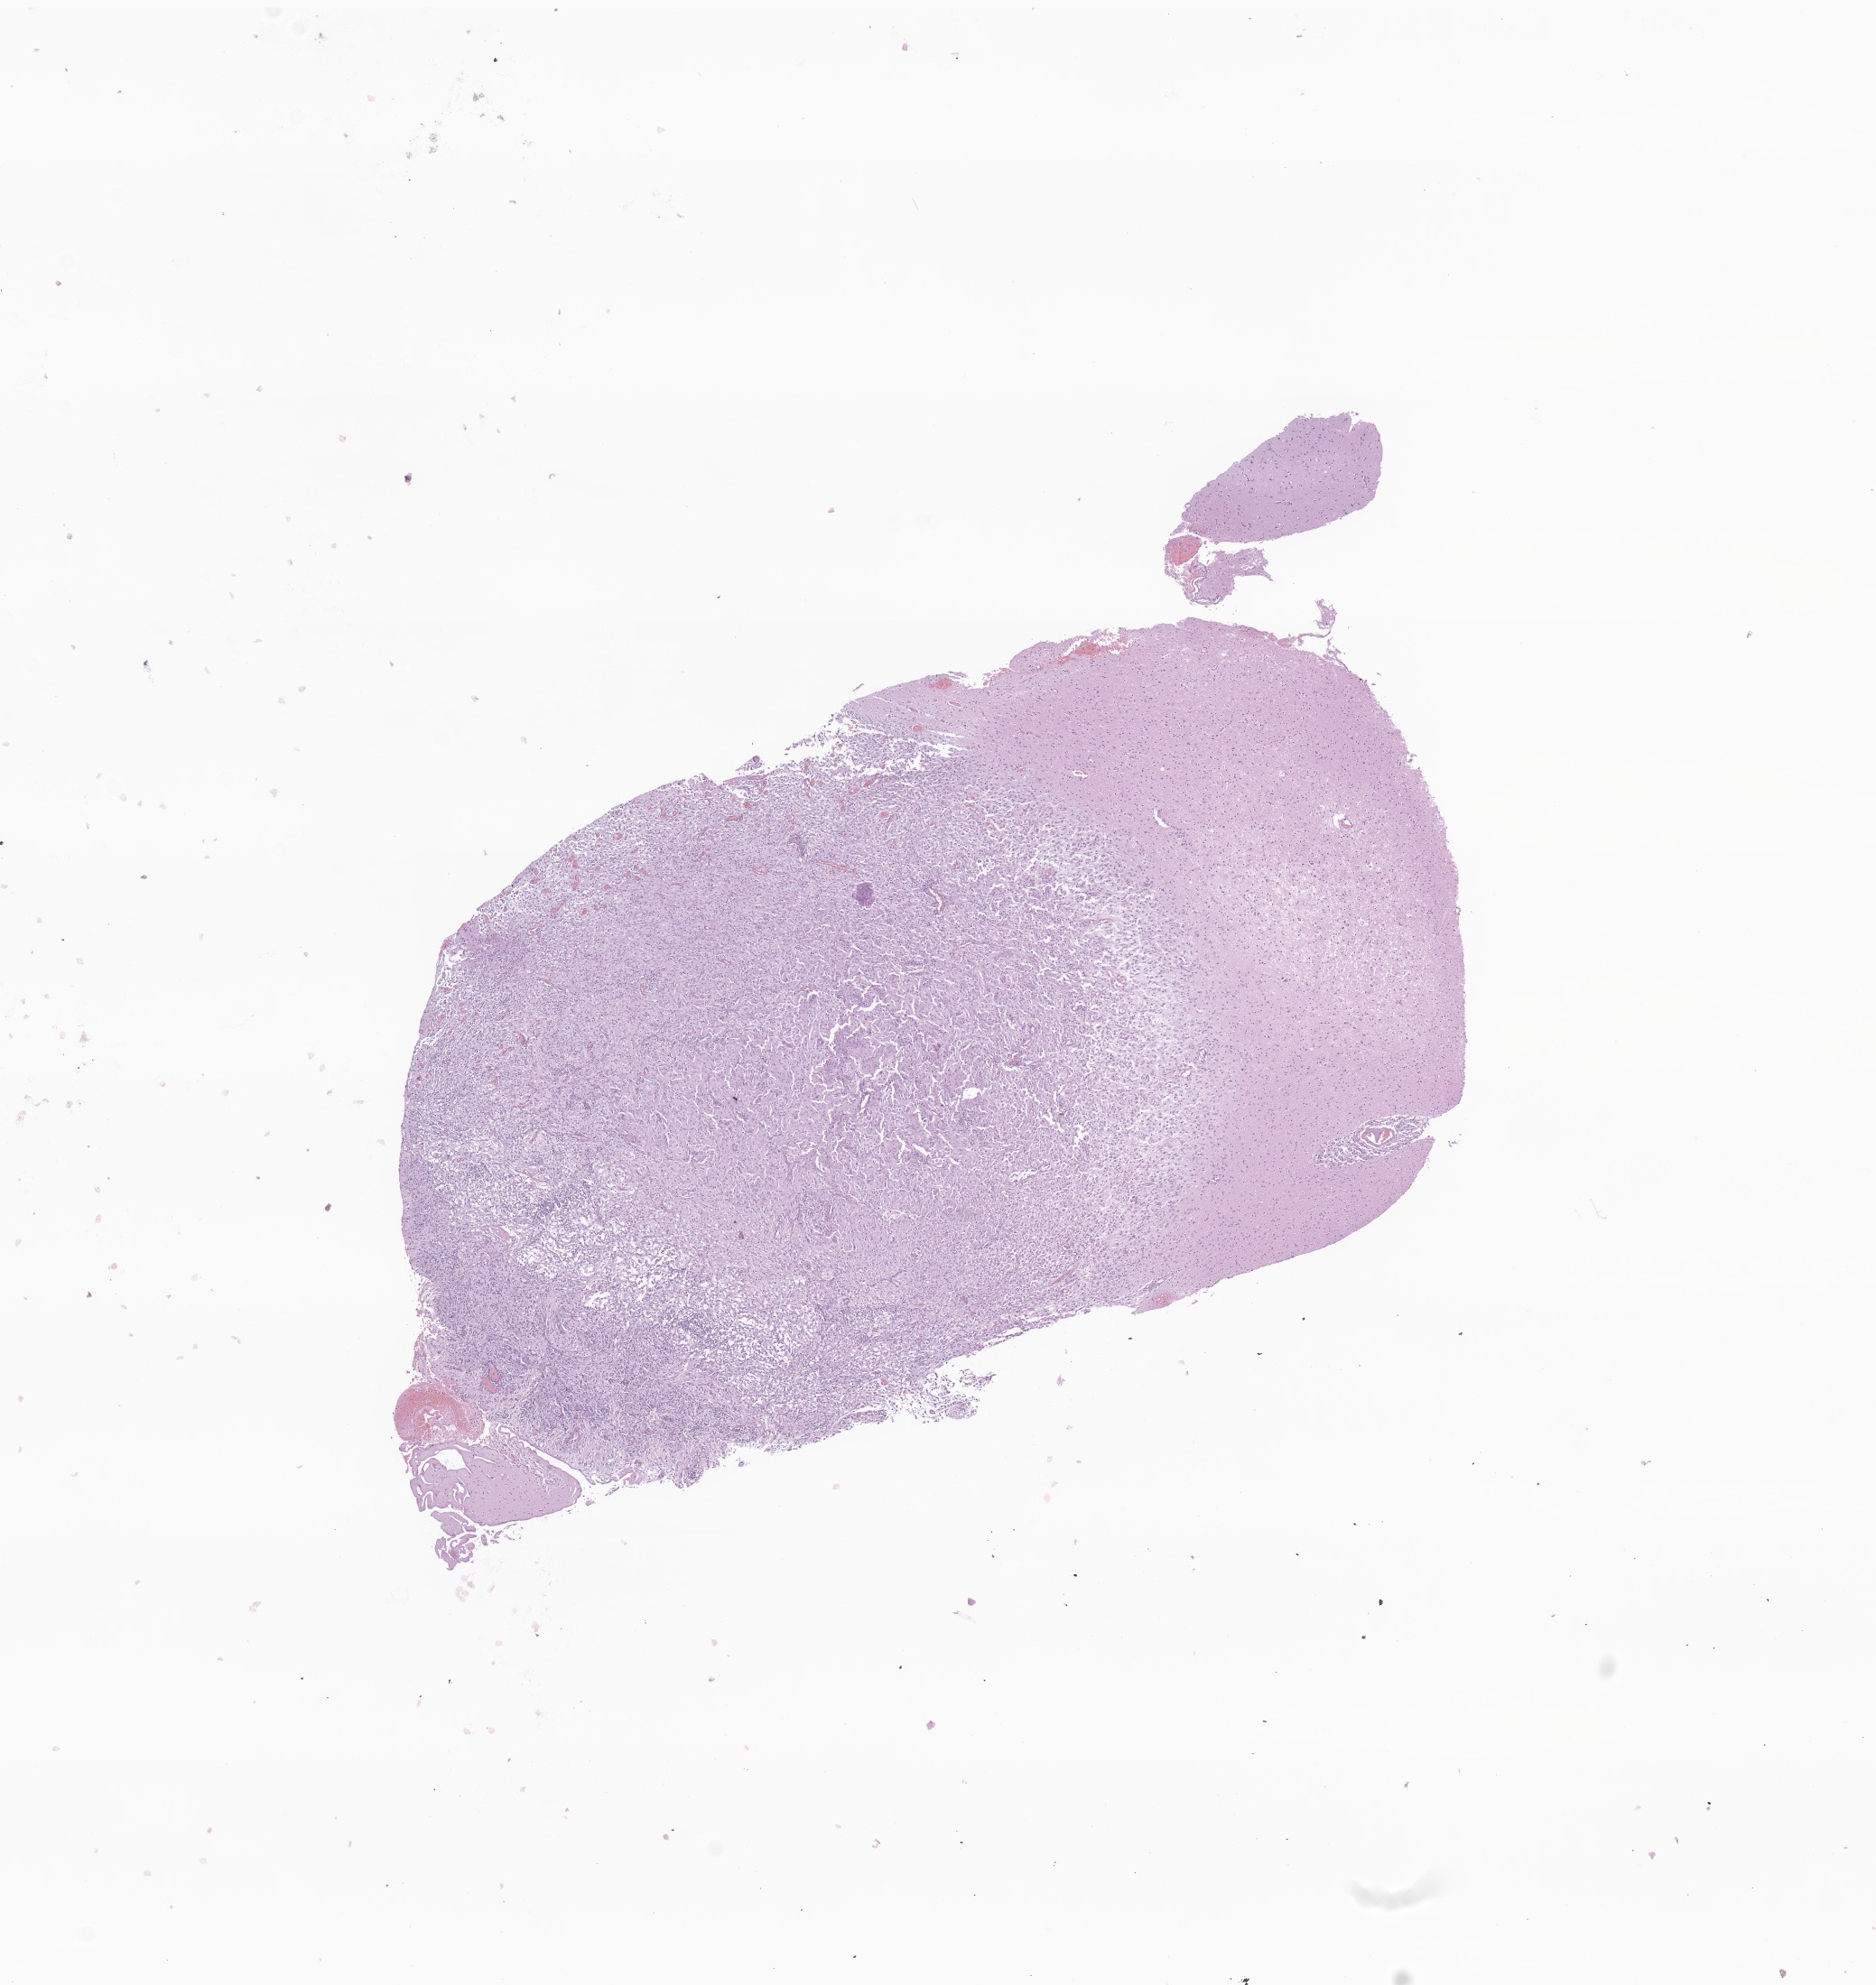
Whole-slide image, H&E stain of tumor tissue from the brain, shown as a low-resolution overview of the whole scanned area (about 8.8 x 9.3 mm). FFPE section. Patient: female, age 161 months (13 years 5 months).
Diagnosis: Neoplasm, uncertain whether benign or malignant.